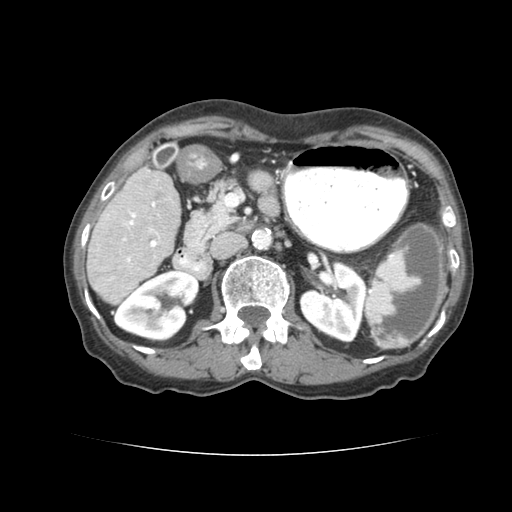
Contrast-enhanced abdominal CT (liver protocol), one axial slice; position 28 of 77 along the scan axis; reconstruction kernel STANDARD; 120 kVp; soft-tissue window (W 400 / L 40 HU); 2.5 mm slice thickness; 512 × 512 image matrix, field of view 340 × 340 mm. From the clinical record (not read from this slice): diagnosis: hepatocellular carcinoma (patient treated with transarterial chemoembolisation; whether this scan precedes or follows treatment is not stated here); TNM stage (as recorded): Stage-I; Child-Pugh class: A; tumour nodularity: uninodular.
Outlined on this slice (semi-automatic segmentation, software-assisted and operator-edited):
- liver parenchyma outside the tumour (the mass and vessels are separate outlines, so this box may not span the whole liver): bounding box (x1, y1, x2, y2) in pixels: (86, 164, 180, 300)
- liver vessels: (122, 199, 155, 244)